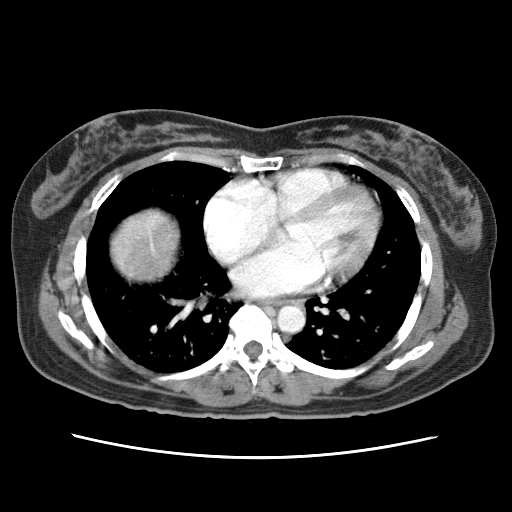
Contrast-enhanced abdominal CT (liver protocol), one axial slice; slice 73 of 79 in the series (ordered by position); 120 kVp; soft-tissue window (W 400 / L 40 HU); 2.5 mm slice thickness; 512 × 512 image matrix. Case-level facts recorded for this patient, not image findings: diagnosis: hepatocellular carcinoma (patient treated with transarterial chemoembolisation; whether this scan precedes or follows treatment is not stated here); TNM stage (as recorded): Stage-I; Child-Pugh class: A; tumour differentiation: moderately differentiated; tumour nodularity: uninodular.
Annotated regions visible in this slice (semi-automatically segmented with operator editing):
- abdominal aorta: bounding box <276,305,303,333> (left, top, right, bottom; pixels)
- liver parenchyma outside the tumour (the mass and vessels are separate outlines, so this box may not span the whole liver): <112,210,178,279>